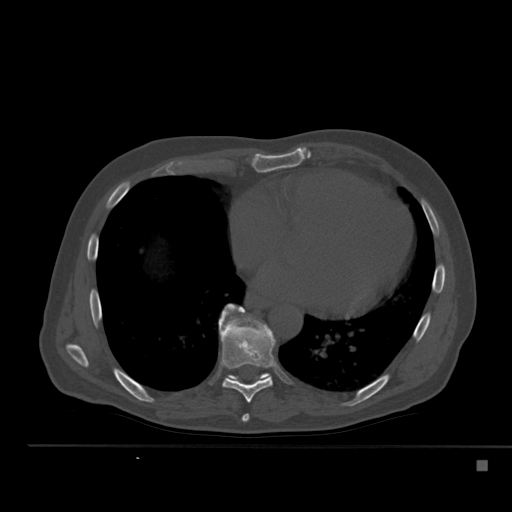
CT including the spine, one axial slice; position 304 of 517 along the scan axis; reconstruction kernel Br40s; 120 kVp; bone window (W 1800 / L 400 HU); 1.5 mm slice thickness; 512 × 512 image matrix, field of view 408 × 408 mm. Male patient, age 70 years. Case-level facts recorded for this patient, not image findings: primary cancer: renal; vertebrae with lytic lesions (as recorded): T4, T6, T10, T12, L3, L4, L5.
Structures marked on this image (semi-automatic segmentation, software-assisted and operator-edited):
- T7 vertebra: box from (x=242, y=414) to (x=250, y=422) px
- T8 vertebra: (x=219, y=304)–(x=276, y=403)
- T9 vertebra: (x=226, y=305)–(x=271, y=383)